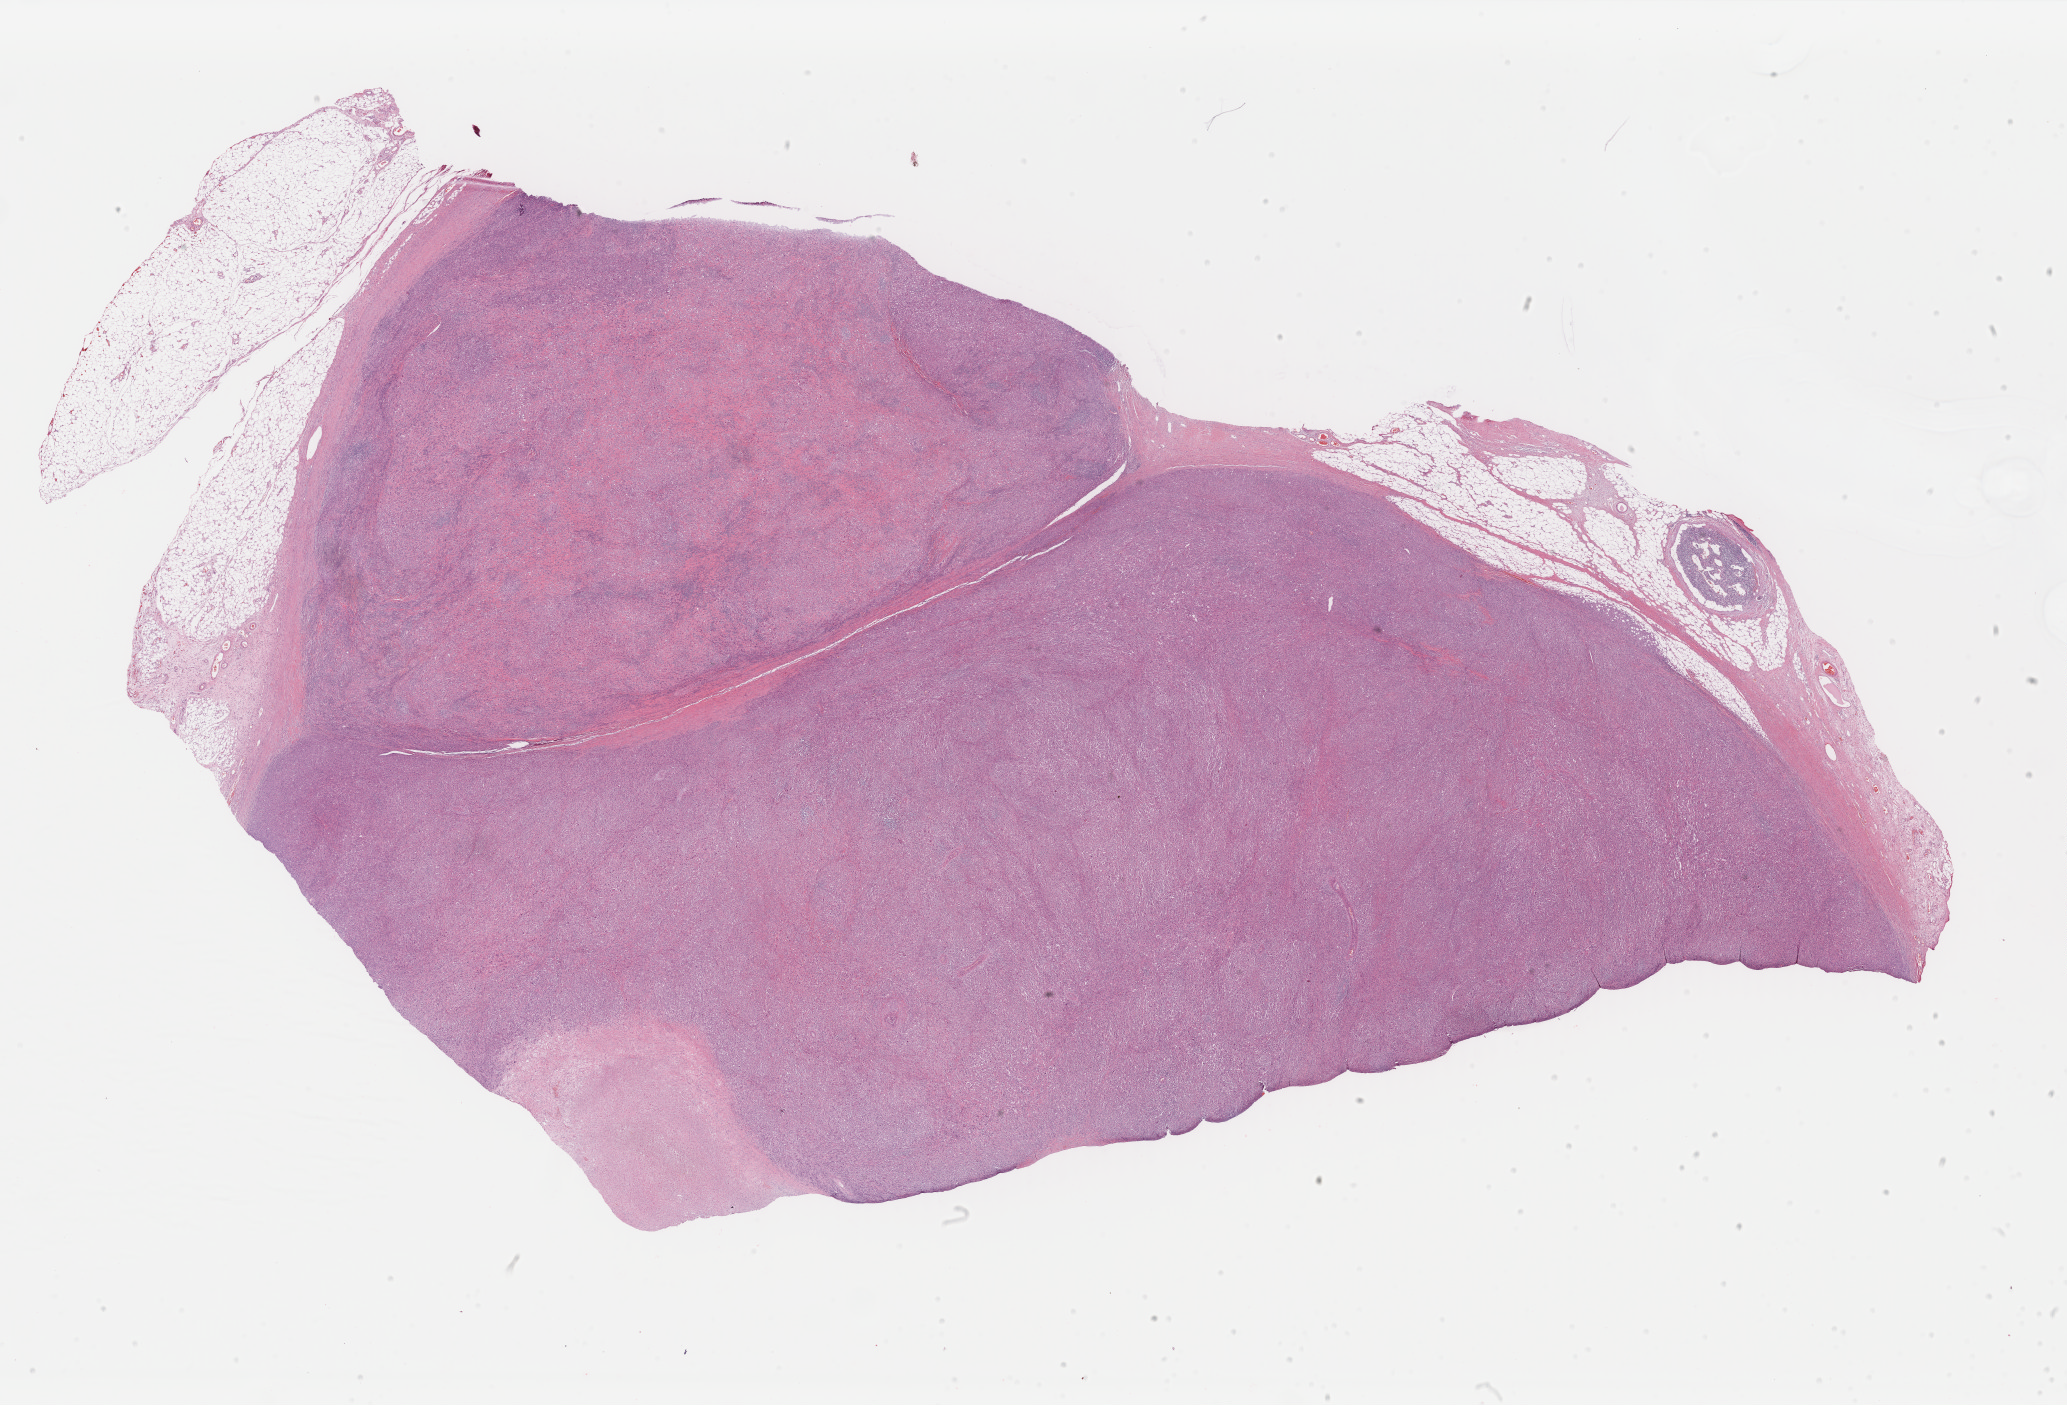
Digitized H&E tissue section (whole slide), whole scanned area (about 32.8 x 22.3 mm, slide scanned at 40x) shown as a low-resolution overview. Formalin-fixed paraffin-embedded (FFPE) diagnostic section. Sample: primary tumour, skin. Male patient; age at initial diagnosis 53 years.
* pathologic diagnosis: Malignant melanoma, NOS